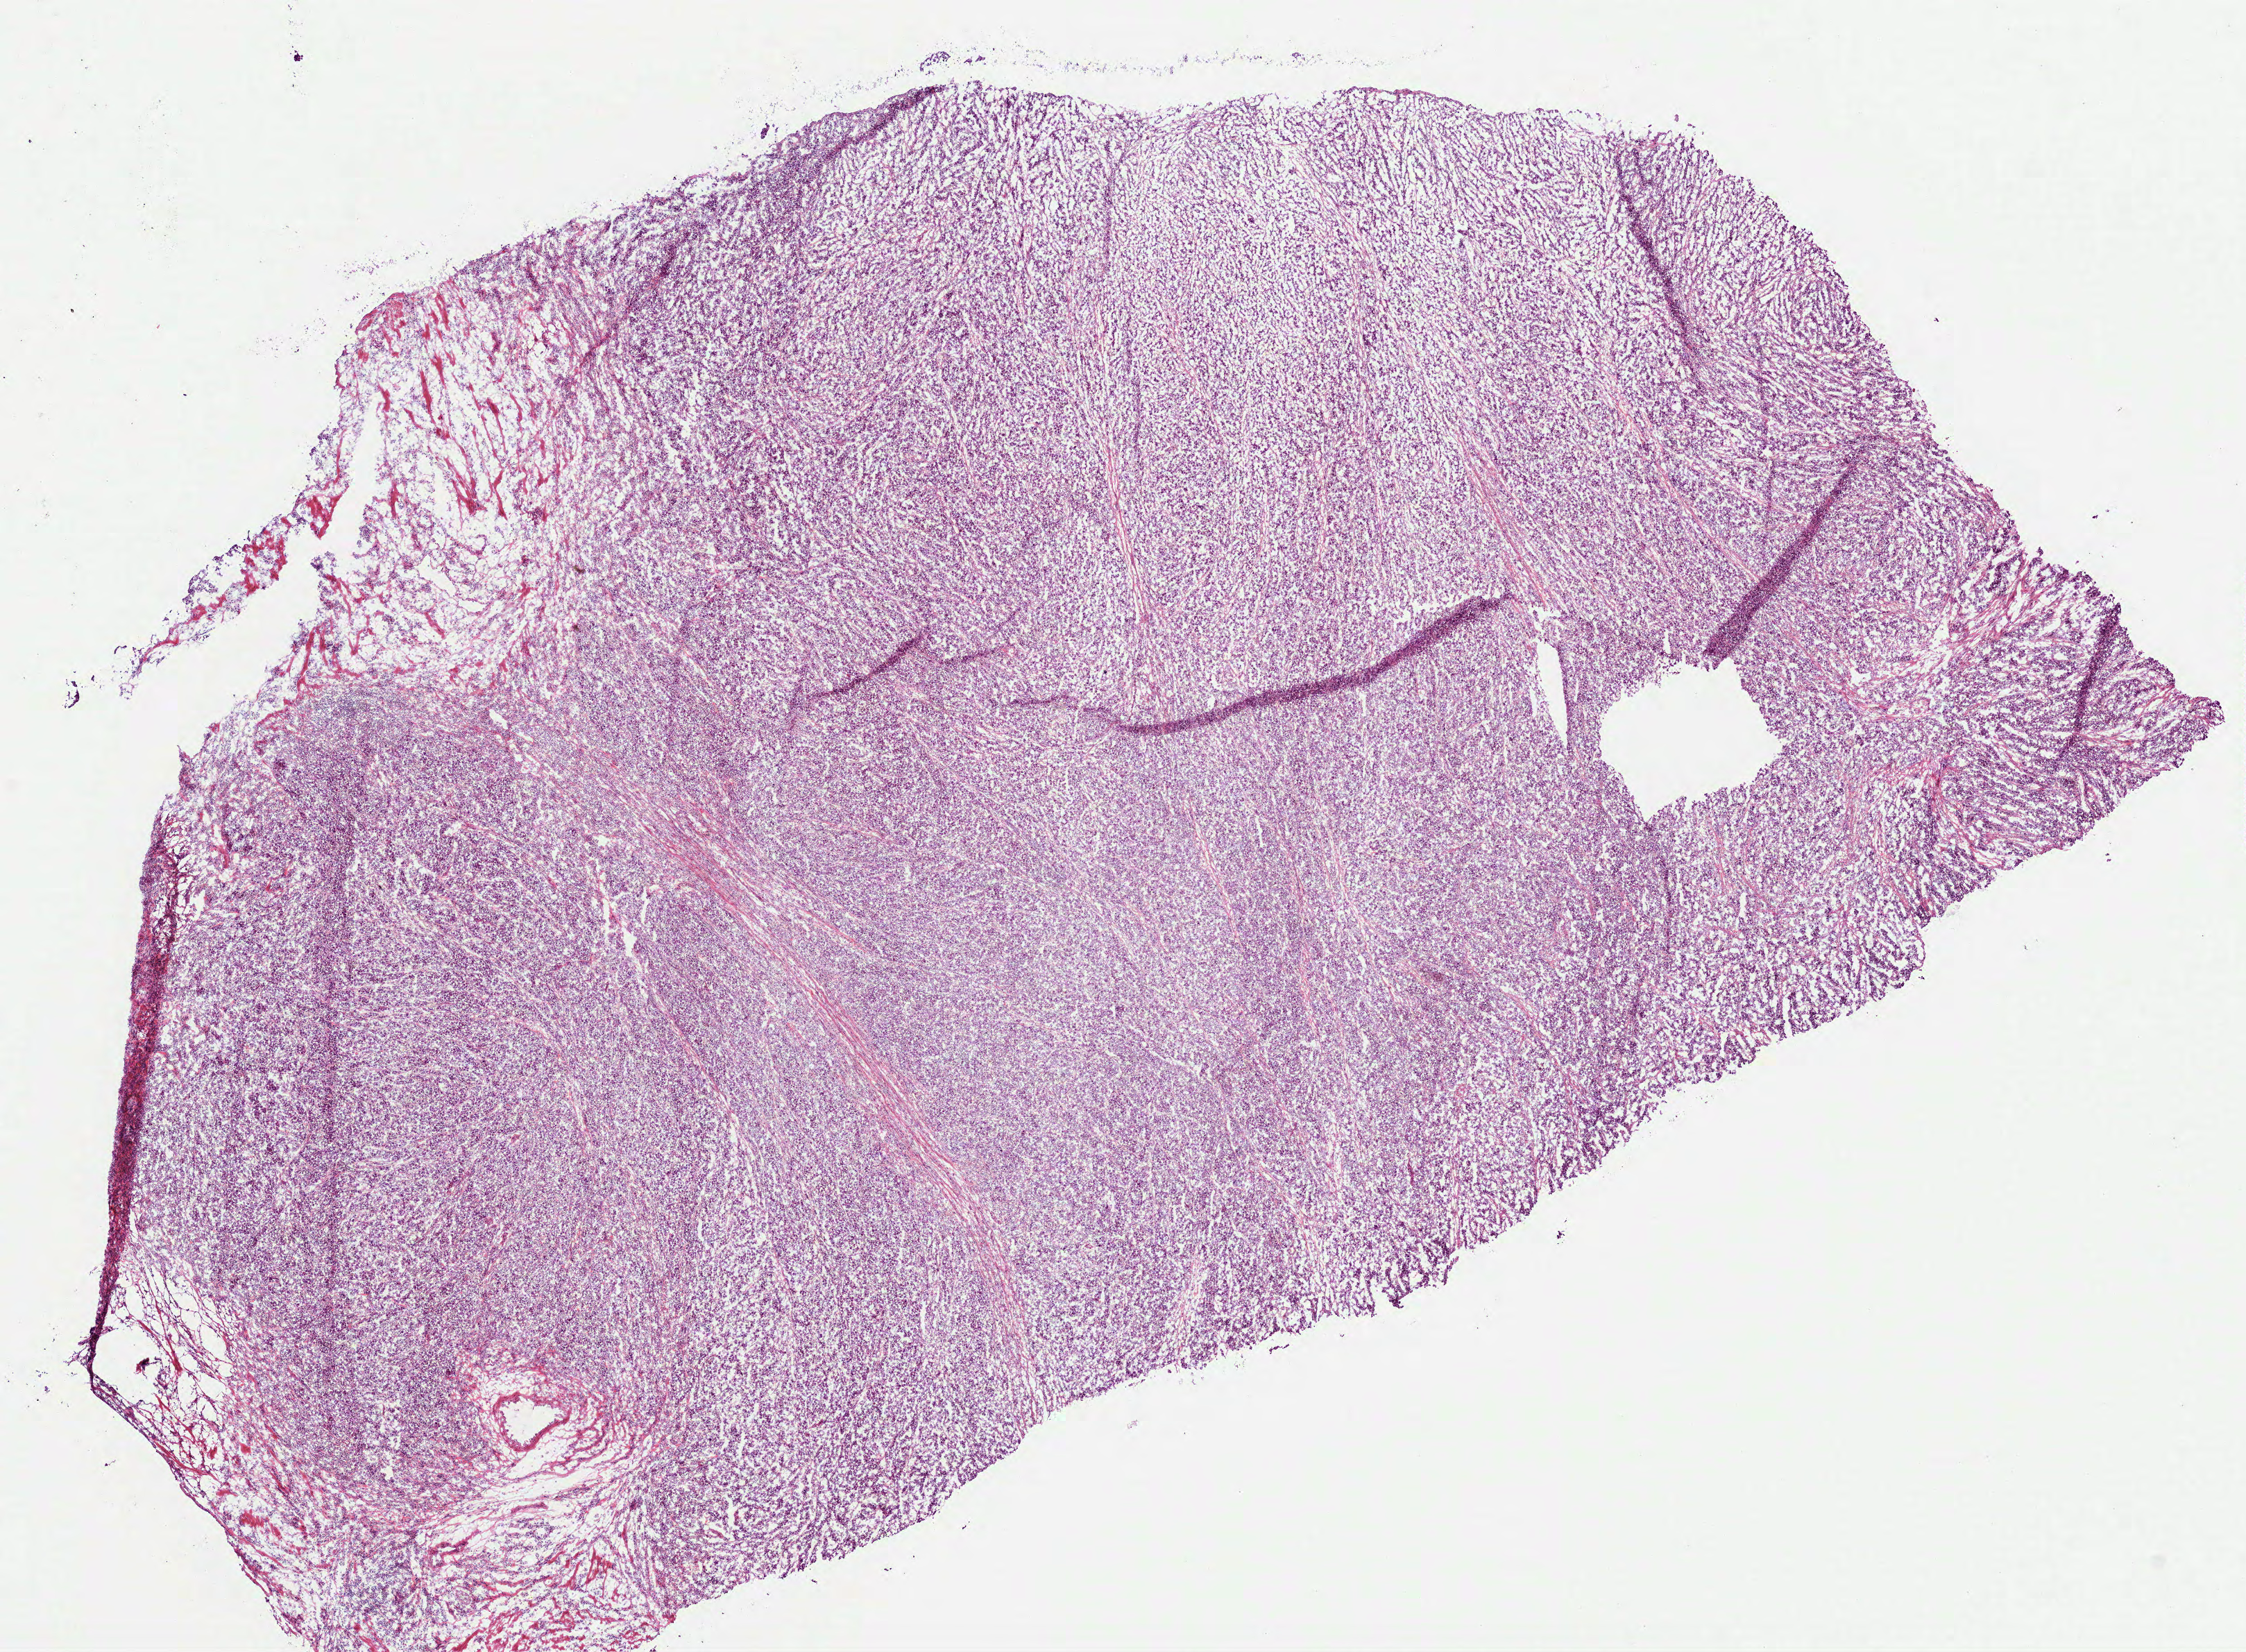
Whole-slide histology image, Hematoxylin and eosin (H&E) stained, low-resolution overview of the scanned area, about 13.1 x 9.6 mm (from a 40x scan), frozen section from the bottom of the tissue portion, primary tumour sample from the stomach. Patient: female, age at initial diagnosis 43 years. Histologic grade: G3 (poorly differentiated). Pathologist review of this section (percent, as recorded): tumour cells 95%, tumour nuclei 90%, normal cells 0%, stromal cells 5%, necrosis 0%.
AJCC pathologic stage: IIIA (6th edition). Diagnosis: Adenocarcinoma, NOS (gastric antrum).